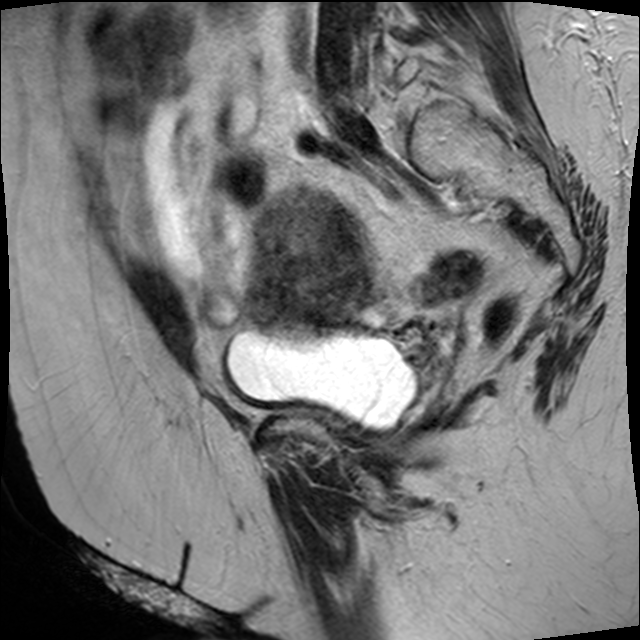
Pelvic MRI for cervical cancer, one sagittal slice; position 29 of 45 along the scan axis; T2-weighted; 1.5 T; TE 89 ms, TR 4610 ms; 4 mm slice thickness; 640 × 640 image matrix, field of view 260 × 260 mm. Patient: female, 50 years.
Outlined on this slice (expert manual segmentation):
- uterus and cervix: bounding box (x1, y1, x2, y2) in pixels: (245, 183, 374, 347)